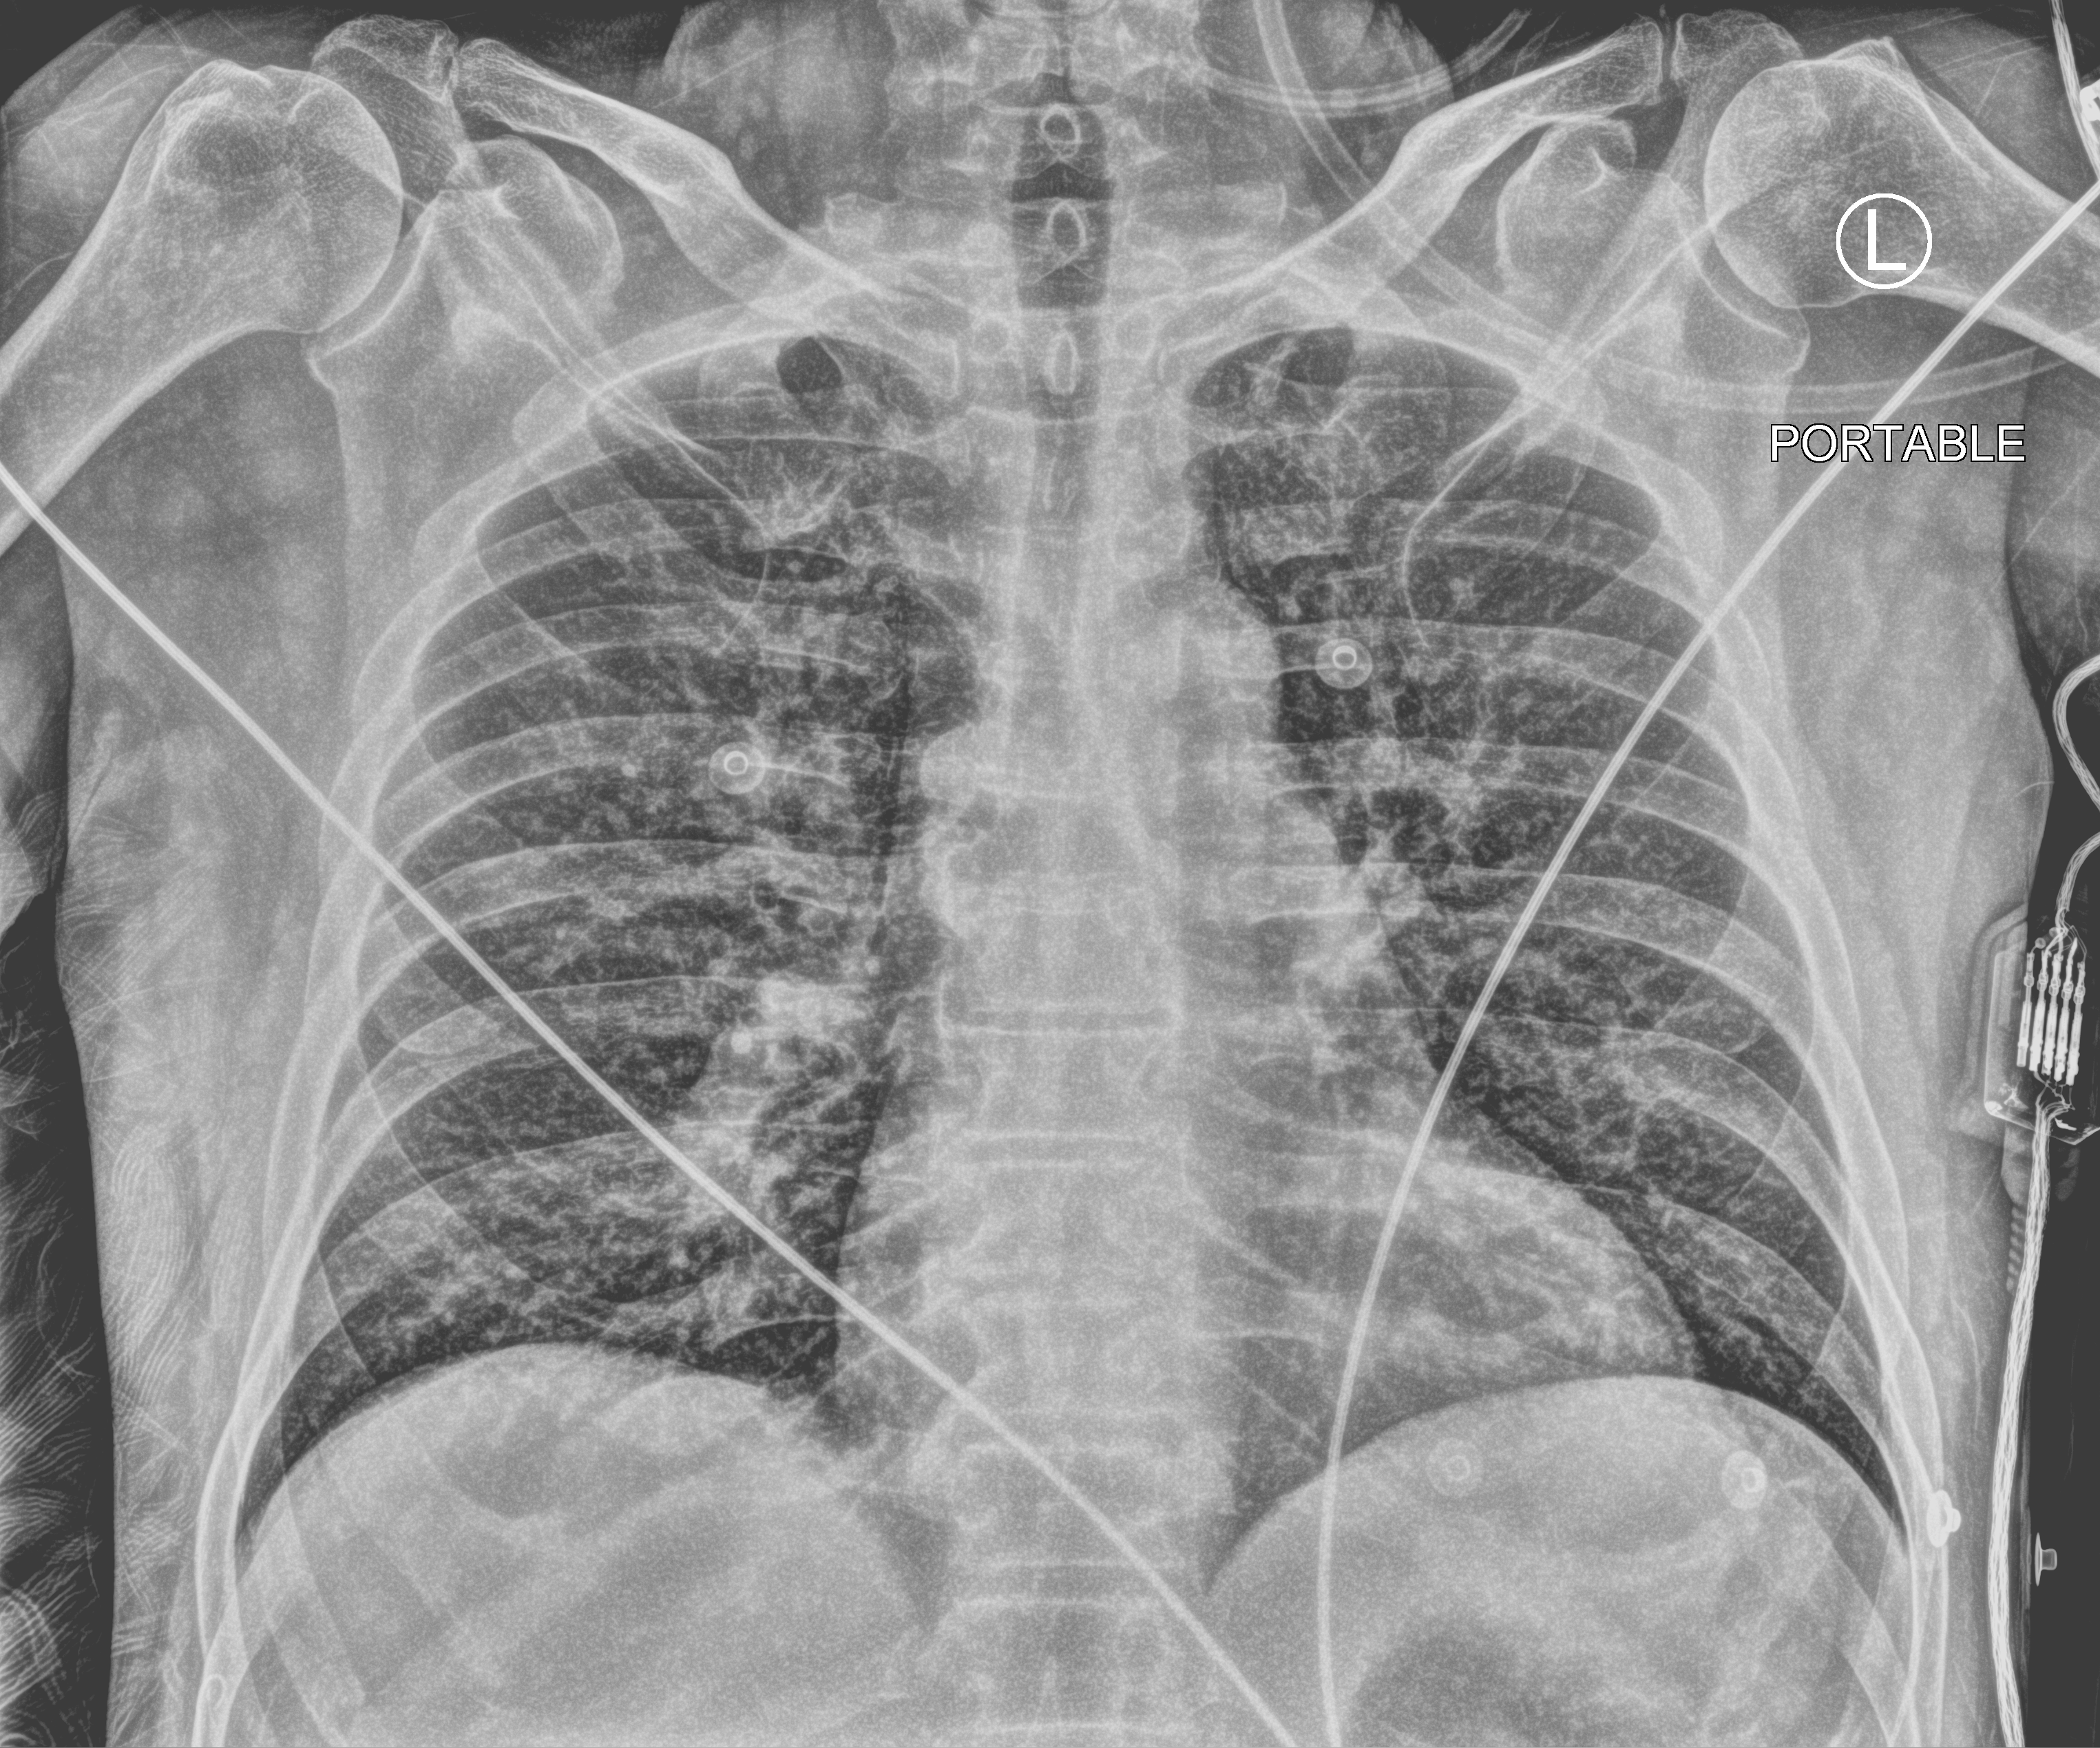
Chest X-ray (portable), anteroposterior (AP) projection. Patient hospitalised with COVID-19; male, aged 18–59 years.
Admission-level facts for this patient (not findings on this image; timing relative to this image not recorded): mechanically ventilated during this hospital stay: no; admitted to intensive care during this hospital stay: no.